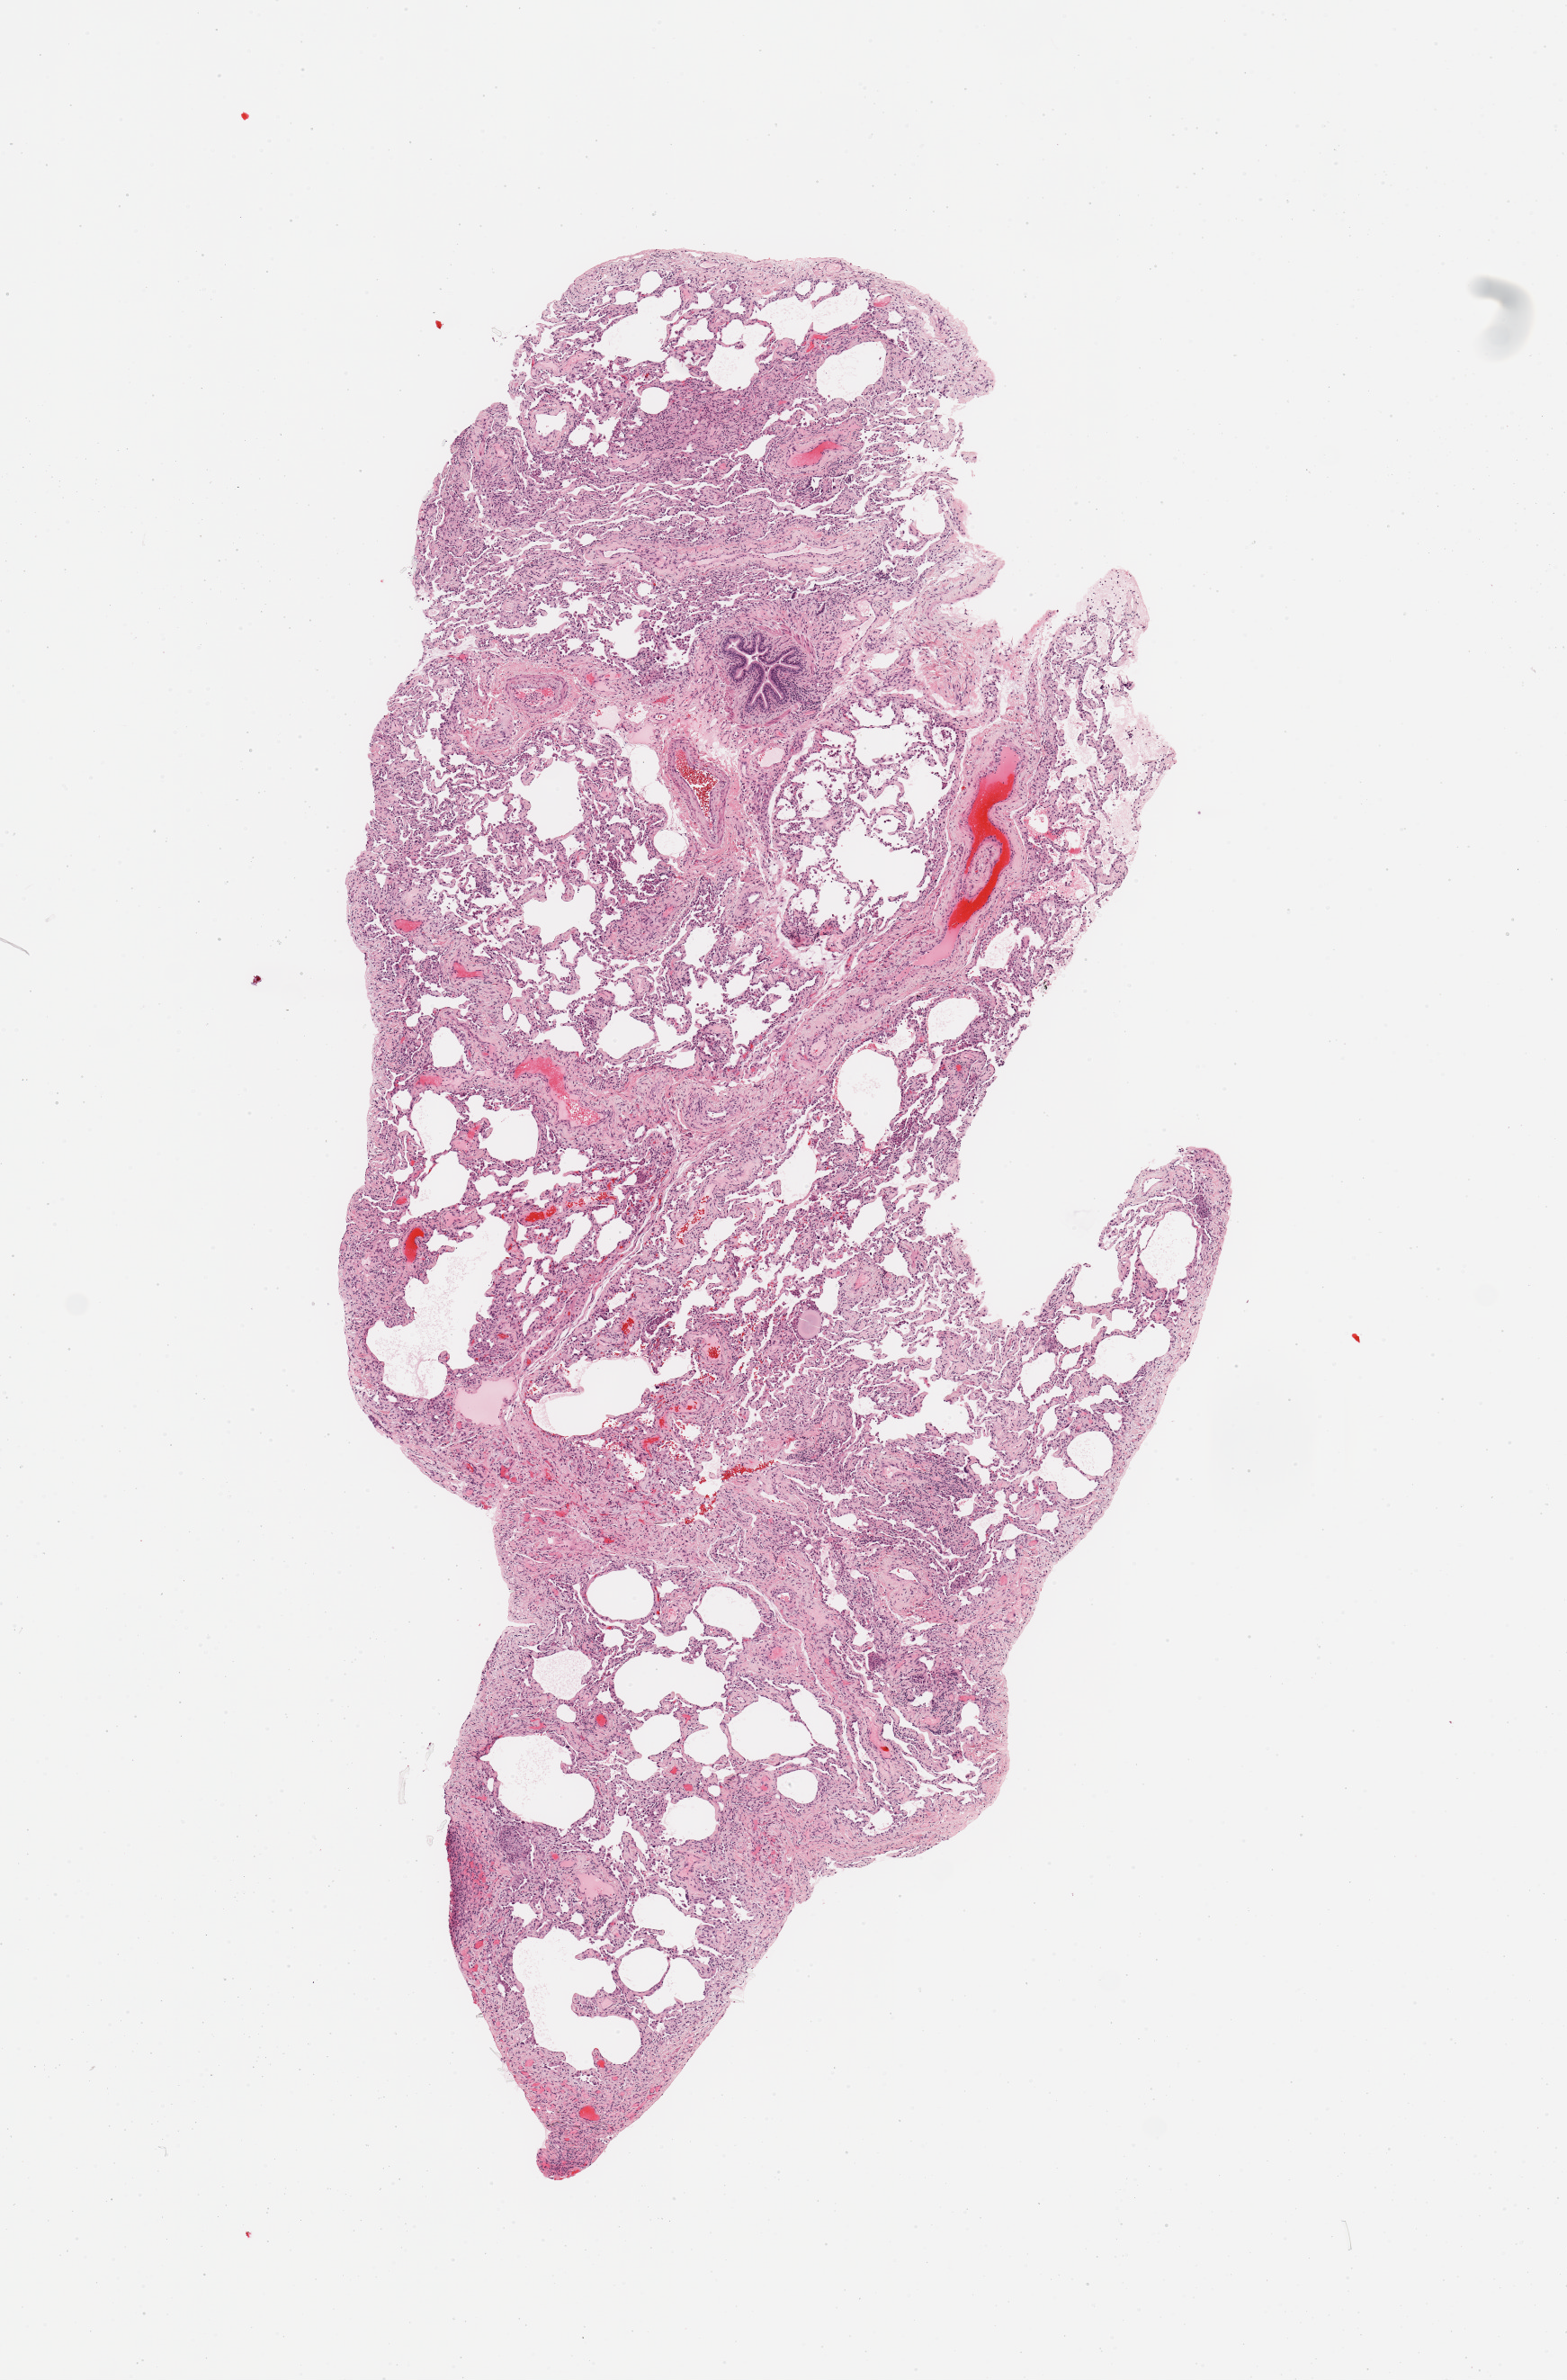
Whole-slide histology image, H&E-stained — whole scanned area (about 6.9 x 10.5 mm, acquisition: 20x scan) shown as a low-resolution overview, normal (non-tumour) tissue sample, sampled site: lung. 66-year-old female patient.
This section: normal (non-tumour) tissue from the same patient. Patient diagnosis: Squamous cell carcinoma, NOS.